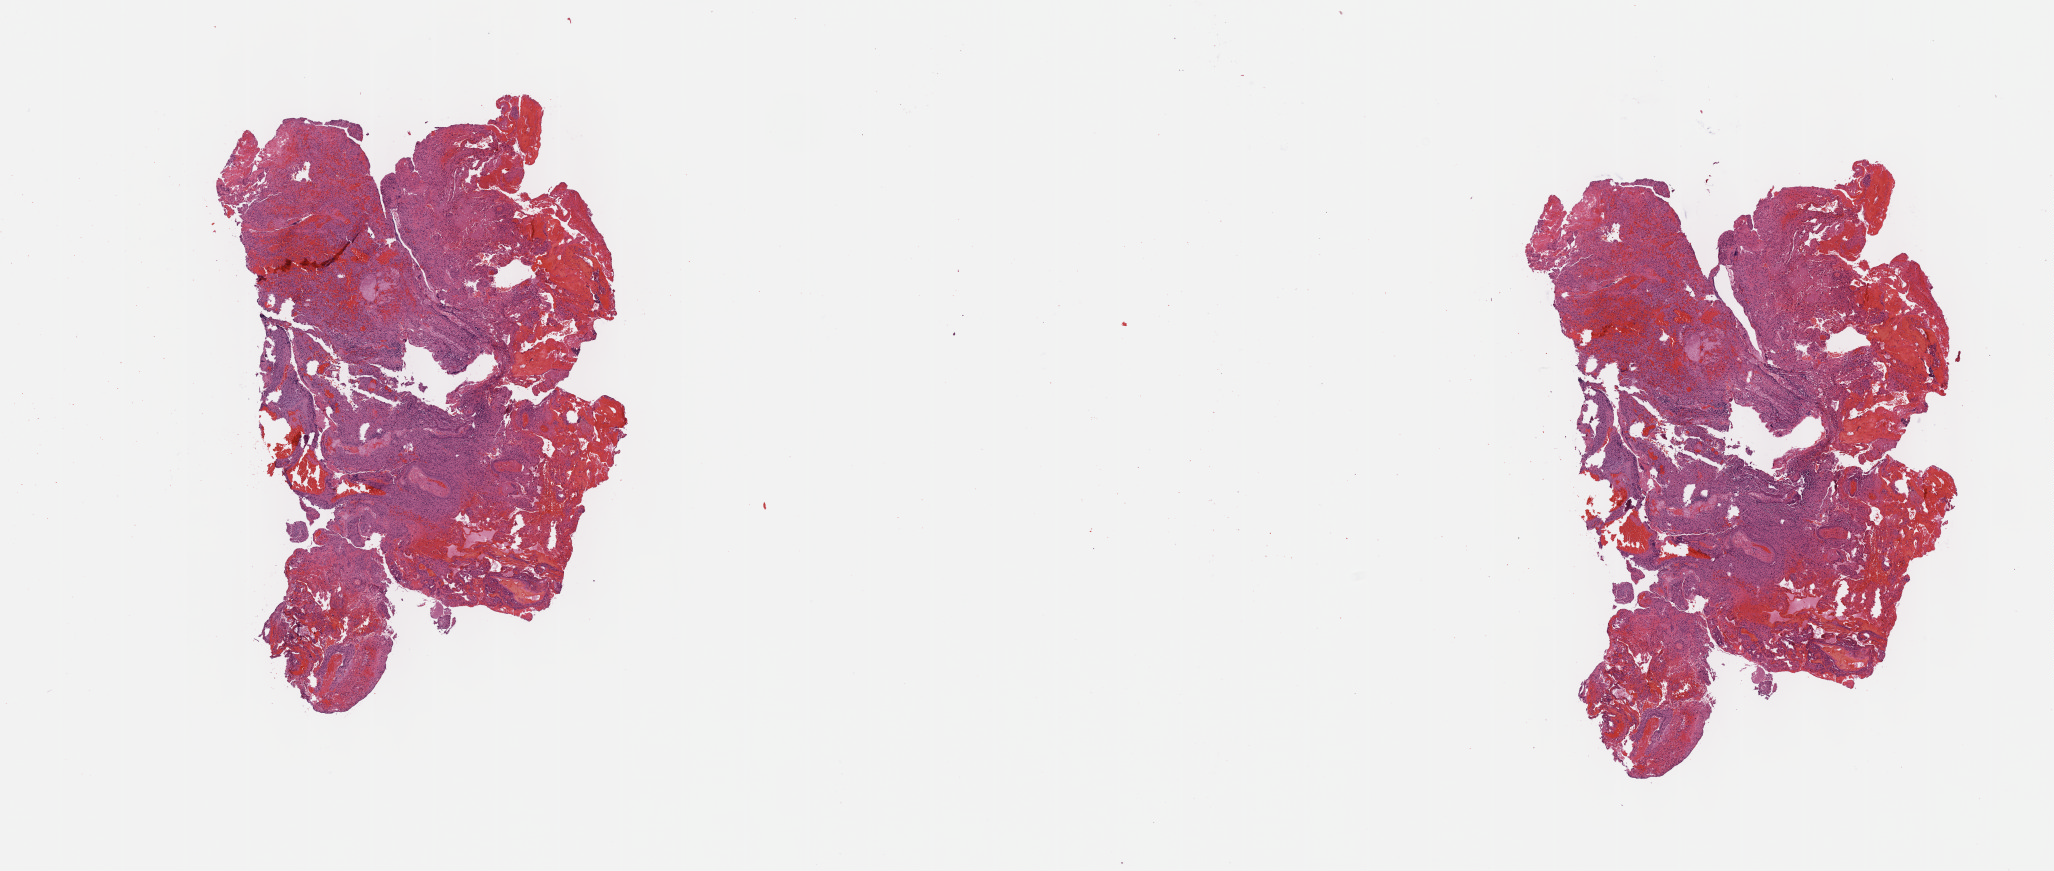
Whole-slide histology image, H&E-stained — low-resolution overview of the scanned area, about 16.6 x 7.0 mm (from a 40x scan), FFPE section, sample: primary tumour, skin. Male, age 71 years at initial diagnosis.
• TNM: TX NX M1c
• AJCC pathologic stage: IV (6th edition)
• diagnosis: Malignant melanoma, NOS